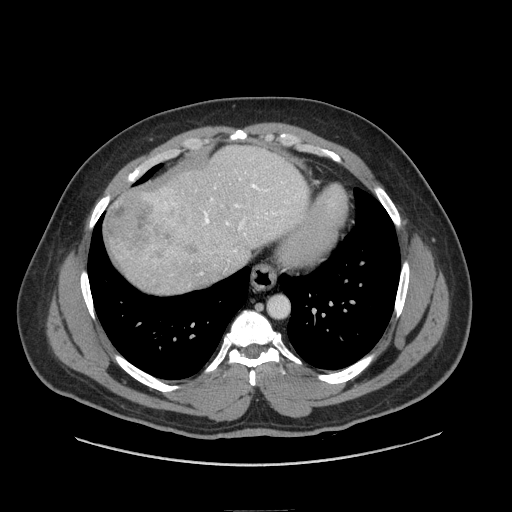
Contrast-enhanced abdominal CT (liver protocol), one axial slice; reconstruction kernel STANDARD; 140 kVp; soft-tissue window (W 400 / L 40 HU); 2.5 mm slice thickness; 512 × 512 image matrix, field of view 440 × 440 mm. Case-level facts recorded for this patient, not image findings: diagnosis: hepatocellular carcinoma (patient treated with transarterial chemoembolisation; whether this scan precedes or follows treatment is not stated here); TNM stage (as recorded): Stage-II; Child-Pugh class: A; tumour differentiation: moderately differentiated.
Annotated regions visible in this slice (semi-automatically segmented with operator editing):
- abdominal aorta: box from (x=268, y=296) to (x=288, y=317) px
- liver parenchyma outside the tumour (the mass and vessels are separate outlines, so this box may not span the whole liver): (x=104, y=146)–(x=308, y=294)
- mass: (x=105, y=190)–(x=199, y=264)
- liver vessels: (x=164, y=184)–(x=276, y=229)